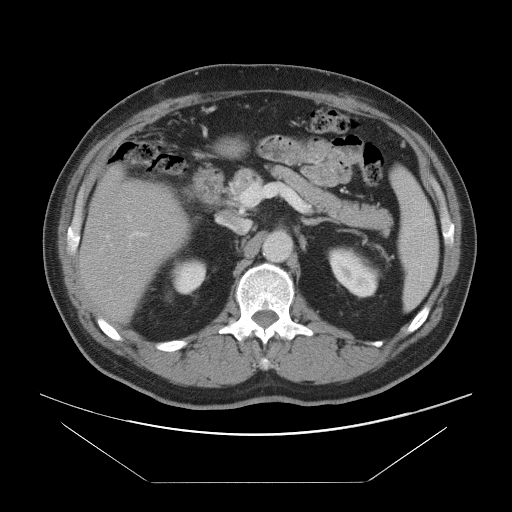
Contrast-enhanced abdominal CT, one axial slice. Slice 48 of 97 in the series (ordered by position). 120 kVp. Intravenous contrast given. Soft-tissue window (W 400 / L 40 HU). 5 mm slice thickness. 512 × 512 image matrix, field of view 442 × 442 mm. Male patient, age 62 years. From the clinical record (not read from this slice): diagnosis: colorectal cancer liver metastases, imaged before liver resection; multiple liver metastases: no; largest metastasis: 7 cm; disease in both lobes: yes.
Annotated regions visible in this slice (expert manual segmentation):
- hepatic veins: bounding box <106,216,131,246> (left, top, right, bottom; pixels)
- liver: <80,171,186,320>
- planned liver remnant (the part of the liver to remain after resection): <80,175,186,320>
- portal vein (with intrahepatic branches): <130,232,147,237>